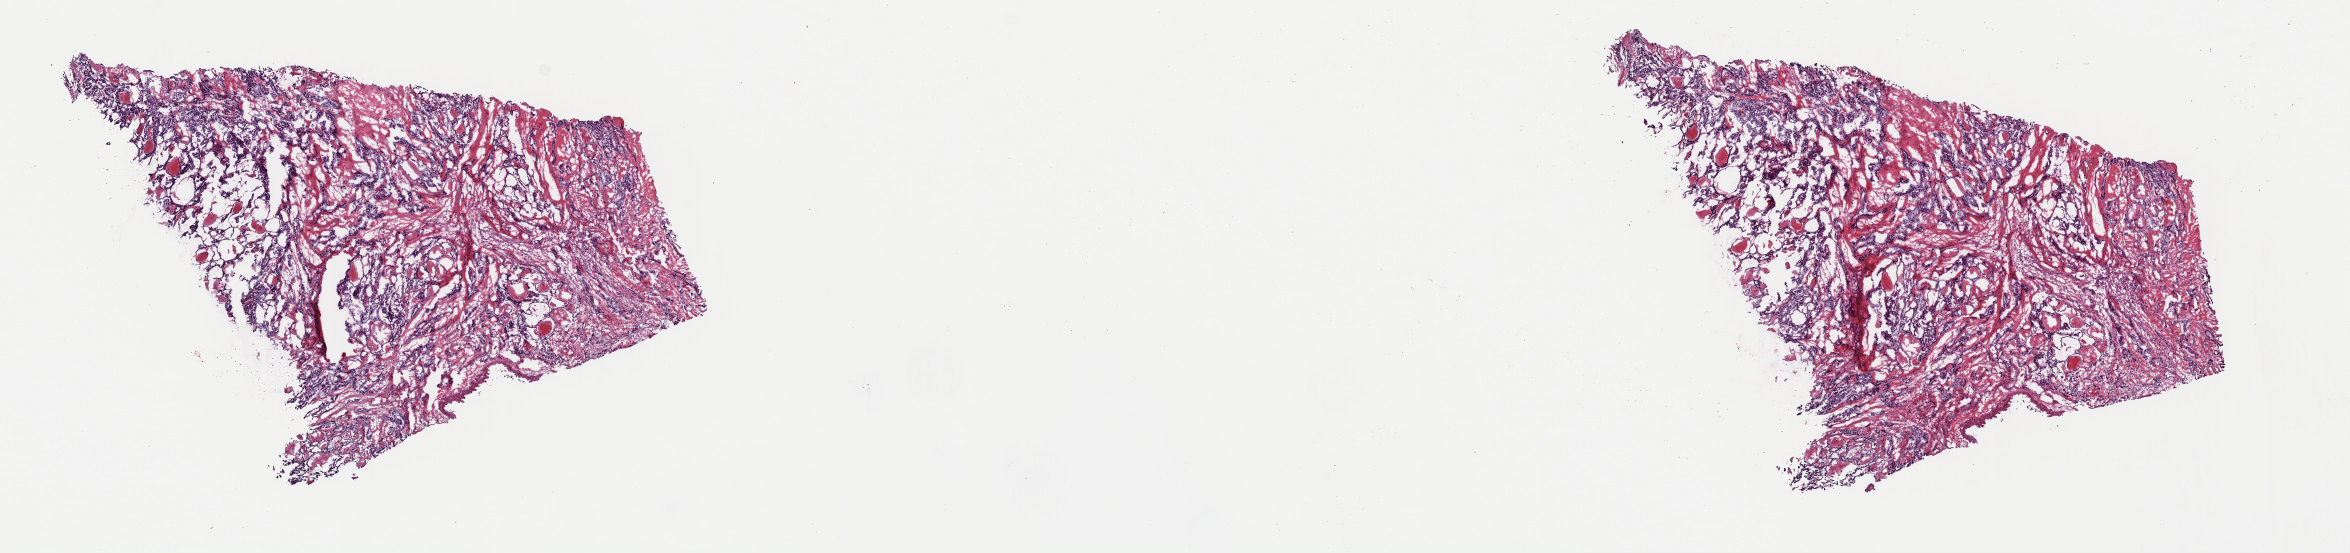
Whole-slide histology image, H&E-stained — whole scanned area (about 18.6 x 4.4 mm, acquisition: 40x scan) shown as a low-resolution overview. Frozen section. Thyroid, primary tumour sample. Female patient; age at initial diagnosis 68 years. Composition of this section per pathologist review: tumour cells 50%, tumour nuclei 75%, normal cells 10%, stromal cells 40%, necrosis 0%. Inflammatory infiltration, as recorded: lymphocyte infiltration 2%, monocyte infiltration 2%, neutrophil infiltration 0%.
Lymph nodes positive (case pathology): 3 of 5 examined. AJCC pathologic stage: III. TNM: T3 N1 M0. Diagnosis: Papillary adenocarcinoma, NOS (thyroid gland).